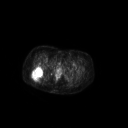
FDG PET of an extremity soft-tissue mass (from a PET/CT study), one axial slice; position 56 of 267 along the scan axis; 3.27 mm slice thickness; 128 × 128 image matrix, field of view 700 × 700 mm. Female patient, age 70 years. From the clinical record (not read from this slice): histological type: synovial sarcoma; grade: intermediate; site of the primary tumour: right buttock.
Outlined on this slice (expert contour drawn on MRI and transferred to this co-registered scan by the dataset authors):
- gross tumour volume including surrounding oedema: box from (x=31, y=66) to (x=44, y=82) px
- gross tumour volume (mass): (x=31, y=66)–(x=44, y=80)